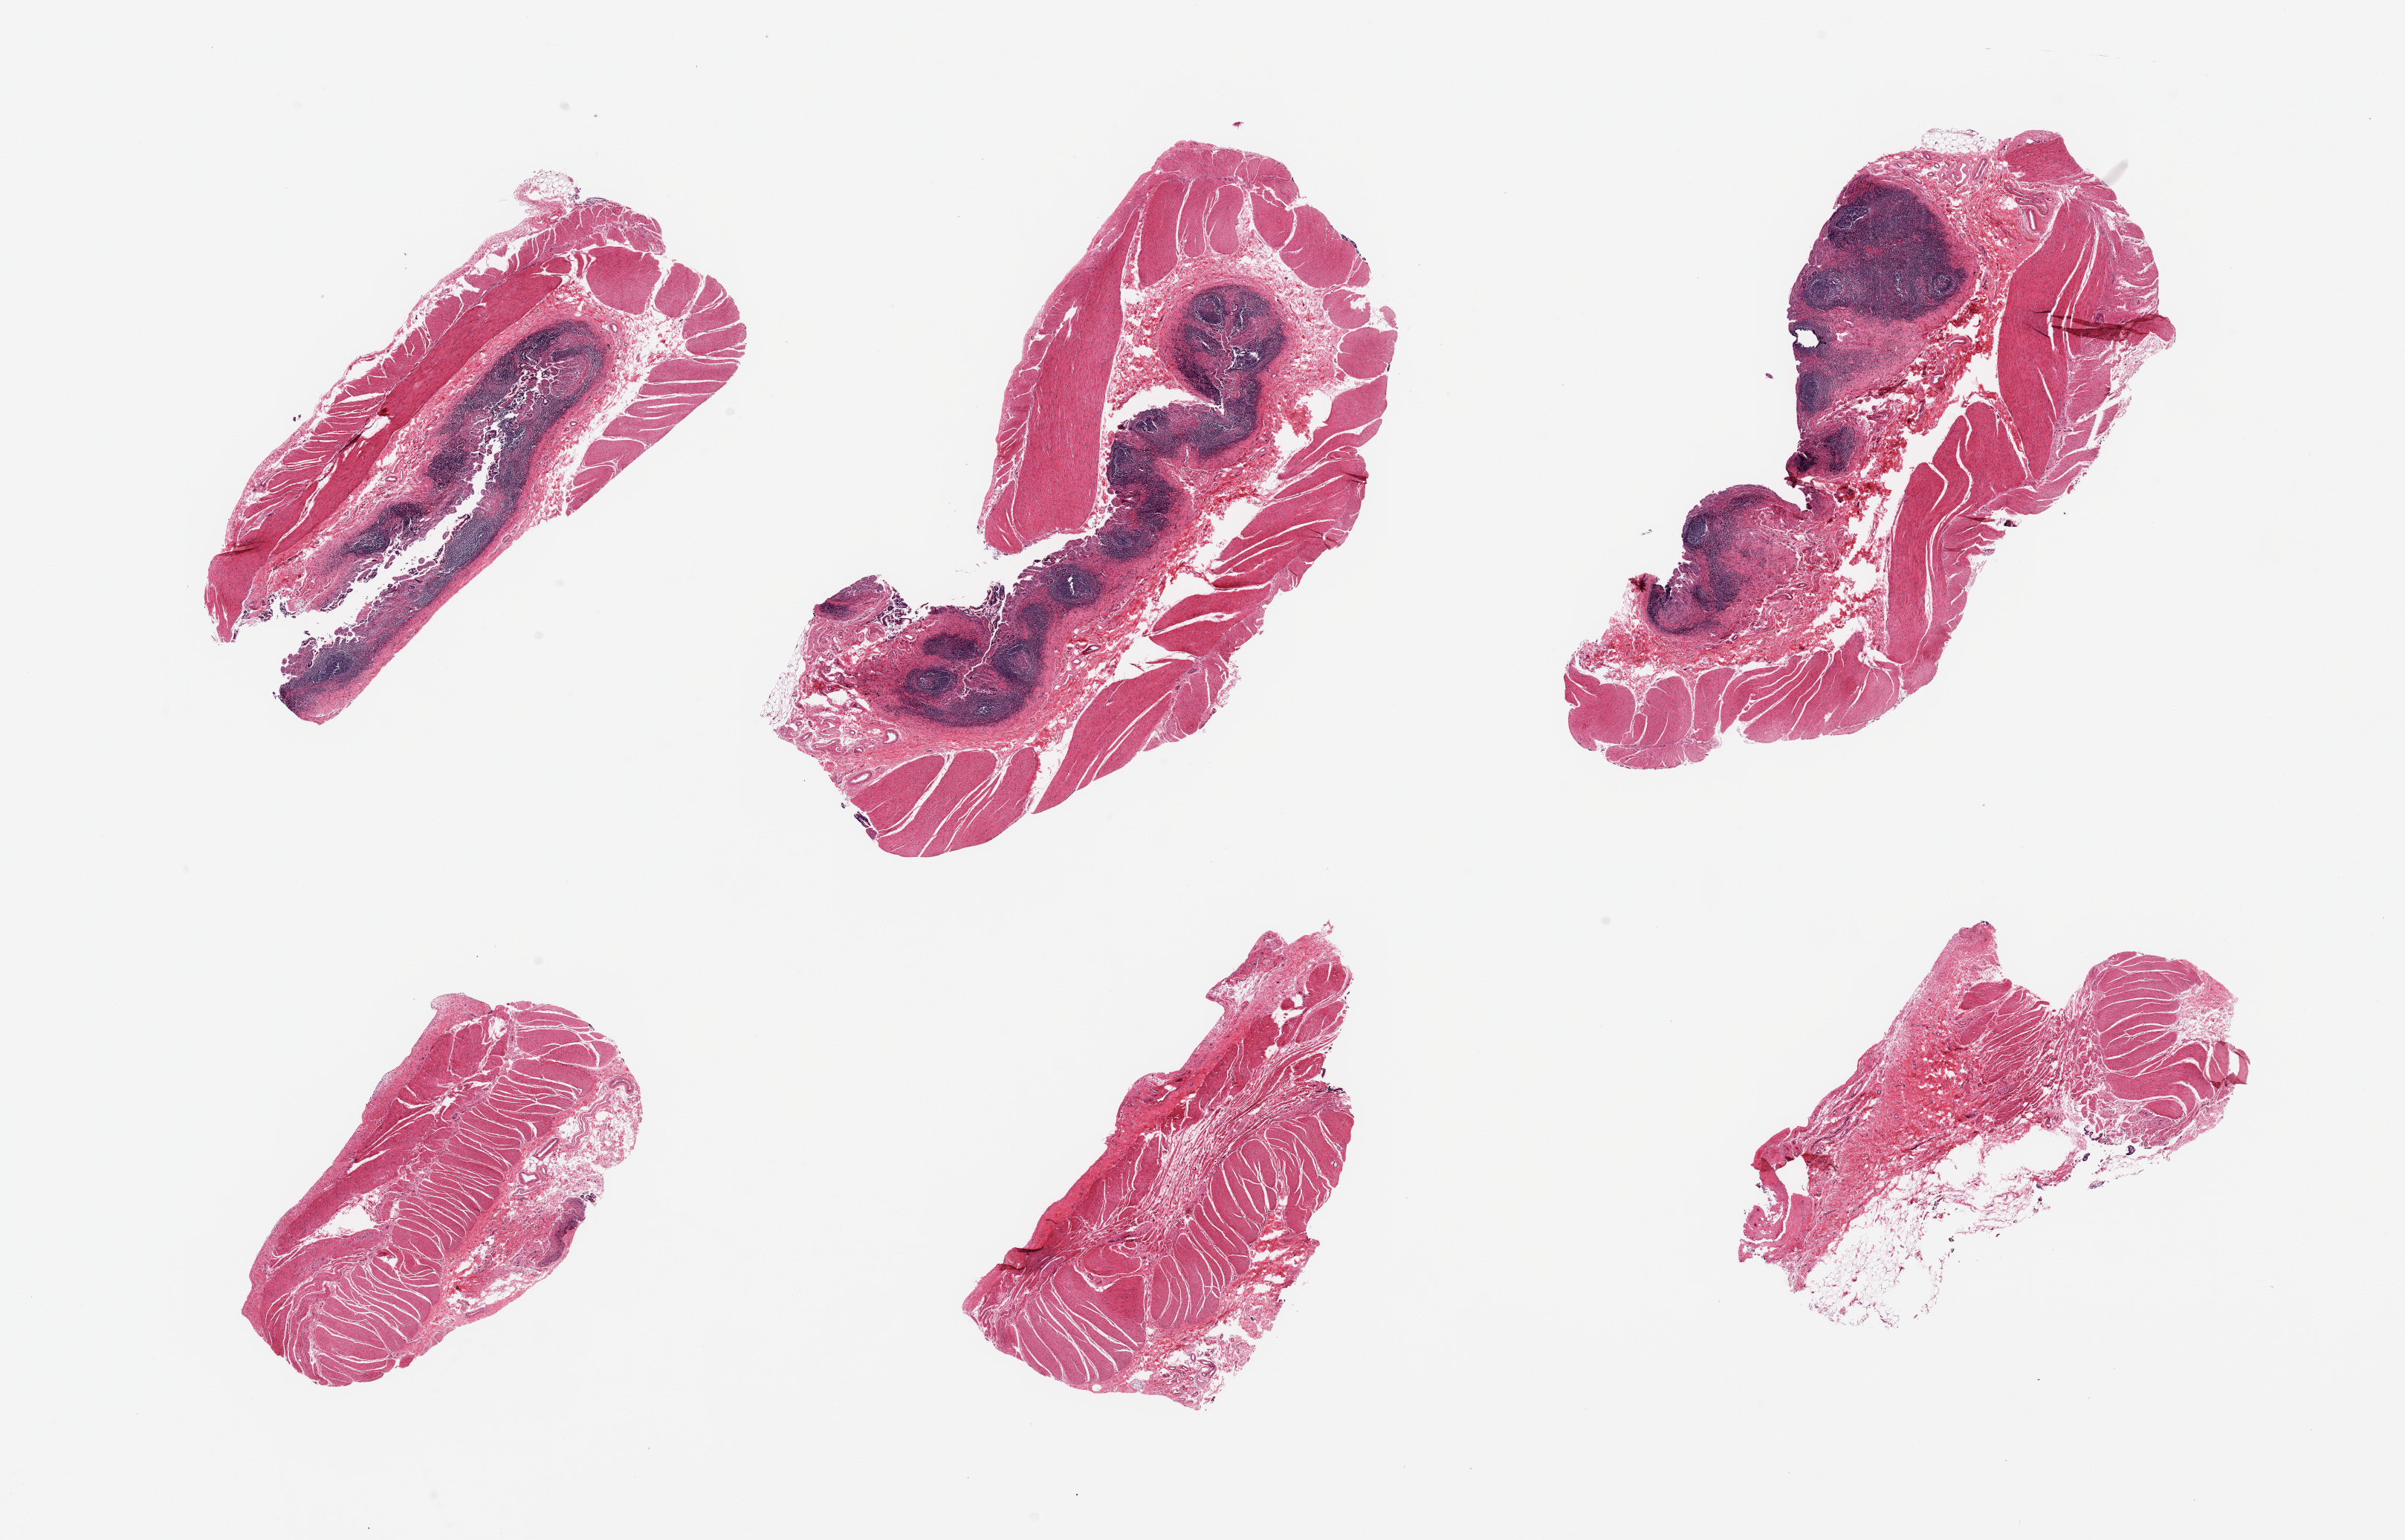
Whole-slide image, hematoxylin and eosin (H&E) stain, brightfield — low-resolution overview of the scanned area, about 25.6 x 16.4 mm (slide scanned at 20x). Donor sex: male.
Specimen: PAXgene-fixed, paraffin-embedded tissue; sampled site (target tissue): ileum; tissue donor sample.